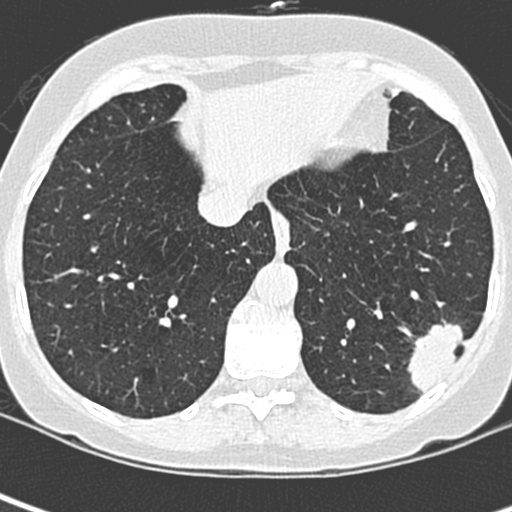
Low-dose screening chest CT, one axial slice; slice 78 of 252 in the series (ordered by position); 120 kVp; lung window (W 1500 / L -600 HU); 512 × 512 image matrix.
Structures marked on this image (expert manual segmentation):
- lesion 1 (tumor, lower lobe of left lung): box from (x=407, y=321) to (x=464, y=394) px